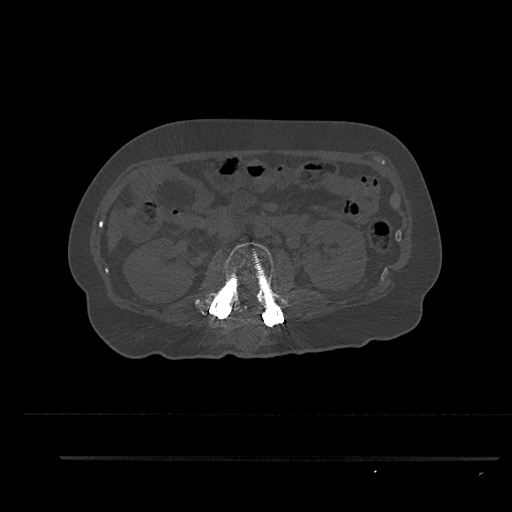
CT including the spine, one axial slice. Slice 164 of 797 in the series (ordered by position). Bone window (W 1800 / L 400 HU). 0.5 mm slice thickness. 512 × 512 image matrix, field of view 408 × 408 mm. Patient: female, 44 years. Case-level facts recorded for this patient, not image findings: primary cancer: renal; vertebrae with lytic lesions (as recorded): L1.
Annotated regions visible in this slice (semi-automatically segmented with operator editing):
- L2 vertebra: bounding box <195,242,286,320> (left, top, right, bottom; pixels)